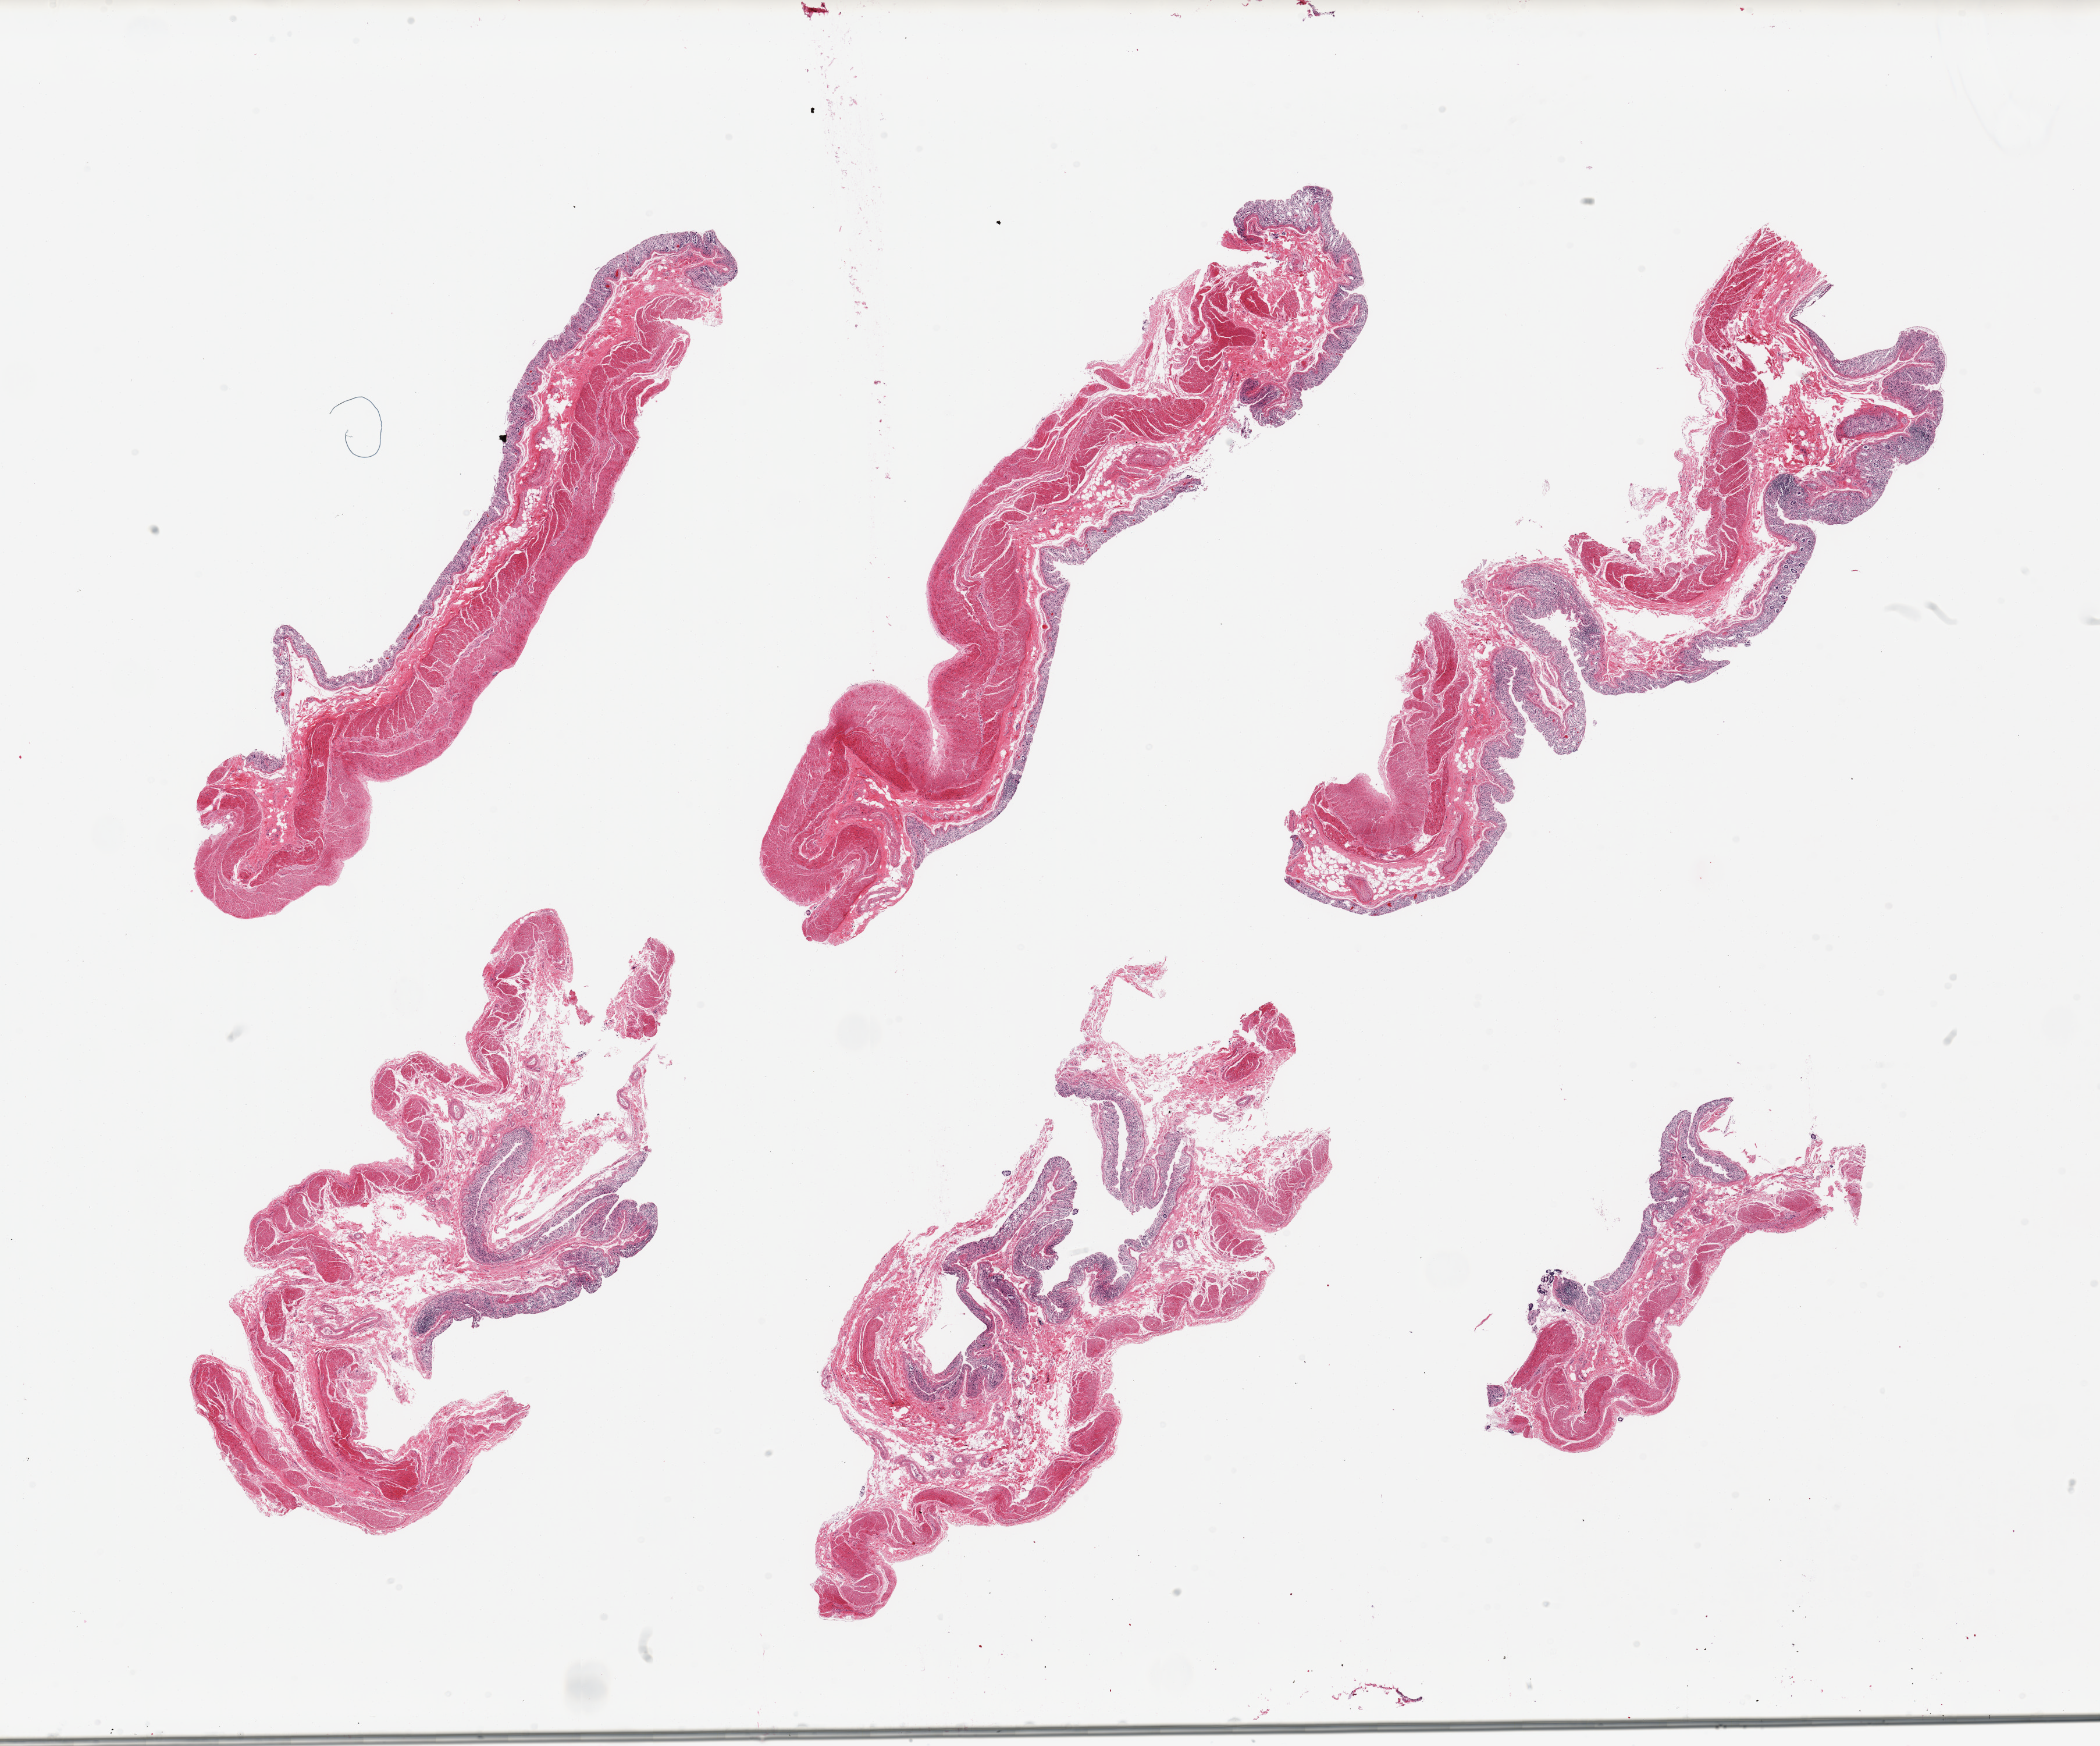
Whole-slide image, haematoxylin and eosin stain, brightfield, whole scanned area (about 28.5 x 23.7 mm) shown as a low-resolution overview, PAXgene-fixed paraffin-embedded (PFPE) section, section of transverse colon (target tissue), tissue donor sample.
Pathologist's review note for this sample: 6 pieces; mucosa largely autolyzed, muscularis better preserved.